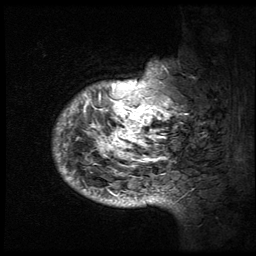
Breast MRI (dynamic contrast-enhanced), one sagittal slice. Position 10 of 64 along the scan axis. 3 images stored at this slice position (order not interpretable as contrast timing). 1.5 T. TE 4.2 ms, TR 9 ms. 256 × 256 image matrix, field of view 180 × 180 mm. Patient: female, 50 years. Case-level facts recorded for this patient, not image findings: setting: breast cancer imaged before/during neoadjuvant chemotherapy; receptor status: triple-negative.
Outlined on this slice (semi-automatic segmentation, software-assisted and operator-edited):
- analysis volume of interest (the breast-tissue region the enhancement analysis was run in; not a lesion): bounding box (x1, y1, x2, y2) in pixels: (53, 40, 194, 212)
- tumour enhancement mask (voxels above the 140 % enhancement threshold inside the analysis volume of interest): (54, 61, 185, 207)